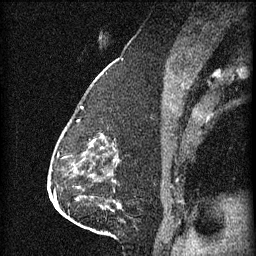
Breast MRI (dynamic contrast-enhanced), one sagittal slice. Slice 31 of 60 in the series (ordered by position). 3 images stored at this slice position (order not interpretable as contrast timing). 1.5 T. TE 4.2 ms, TR 11 ms. 1.5 mm slice thickness. 256 × 256 image matrix. Female patient, age 63 years.
Outlined on this slice (semi-automatically segmented with operator editing):
- analysis volume of interest (the breast-tissue region the enhancement analysis was run in; not a lesion): bounding box <86,120,119,153> (left, top, right, bottom; pixels)
- tumour enhancement mask (voxels above the 70 % enhancement threshold inside the analysis volume of interest): <92,134,103,147>